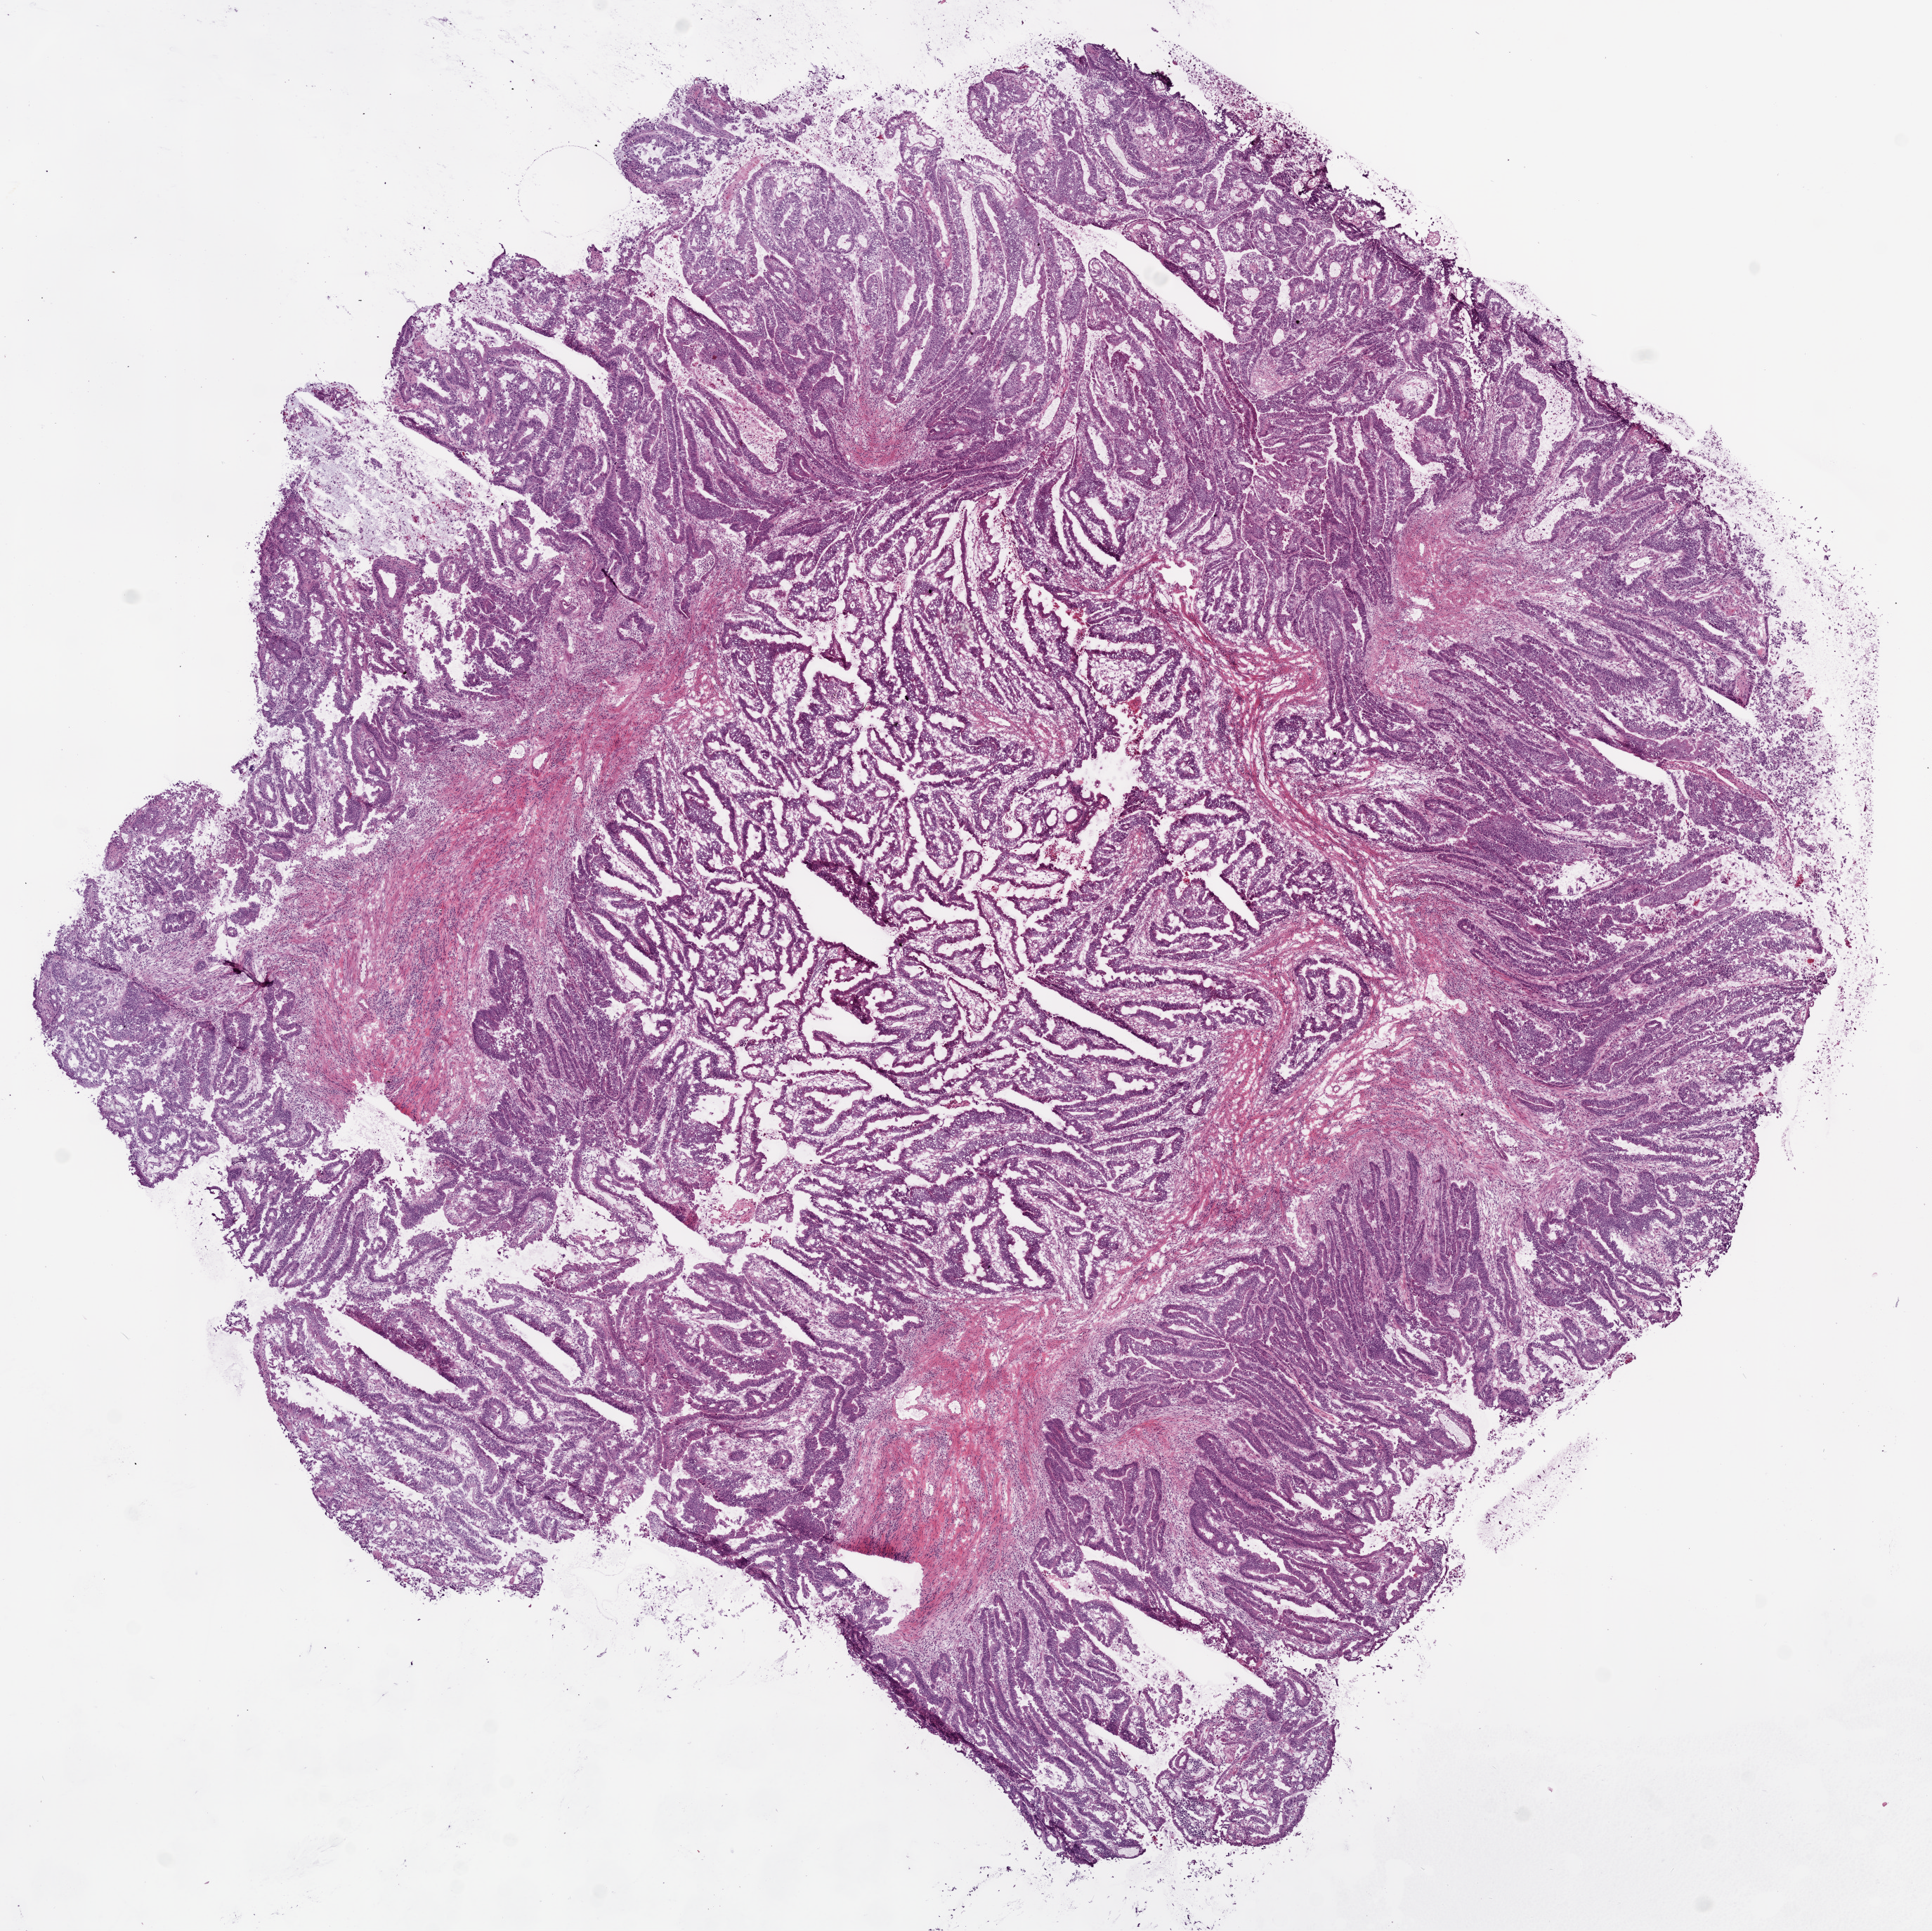
Hematoxylin and eosin (H&E) stained whole-slide image — a low-resolution overview of the entire scanned area, about 11.0 x 11.0 mm; frozen section; sample: primary tumour, rectum. Male patient; age at initial diagnosis 68 years. Pathologist review of this section (percent, as recorded): tumour cells 90%, tumour nuclei 80%, normal cells 0%, stromal cells 9%, necrosis 1%. Inflammatory infiltration, as recorded: lymphocyte infiltration 10%, monocyte infiltration 0%, neutrophil infiltration 5%.
AJCC pathologic stage: I (7th edition). TNM: T1 N0 M0. Histologic diagnosis: Adenocarcinoma, NOS (rectosigmoid junction).